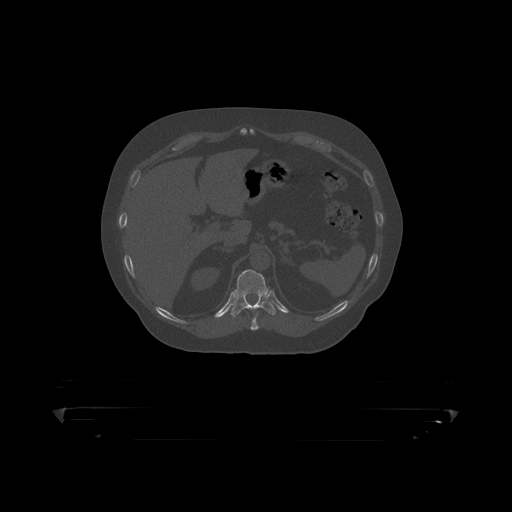
CT including the spine, one axial slice. Position 199 of 390 along the scan axis. 120 kVp. Bone window (W 1800 / L 400 HU). 1.25 mm slice thickness. 512 × 512 image matrix, field of view 650 × 650 mm. Patient: male, 60 years. Case-level facts recorded for this patient, not image findings: primary cancer: prostate.
Outlined on this slice (semi-automatic segmentation, software-assisted and operator-edited):
- T10 vertebra: bounding box [x1, y1, x2, y2] px = [253, 313, 259, 319]
- T11 vertebra: [230, 270, 288, 316]